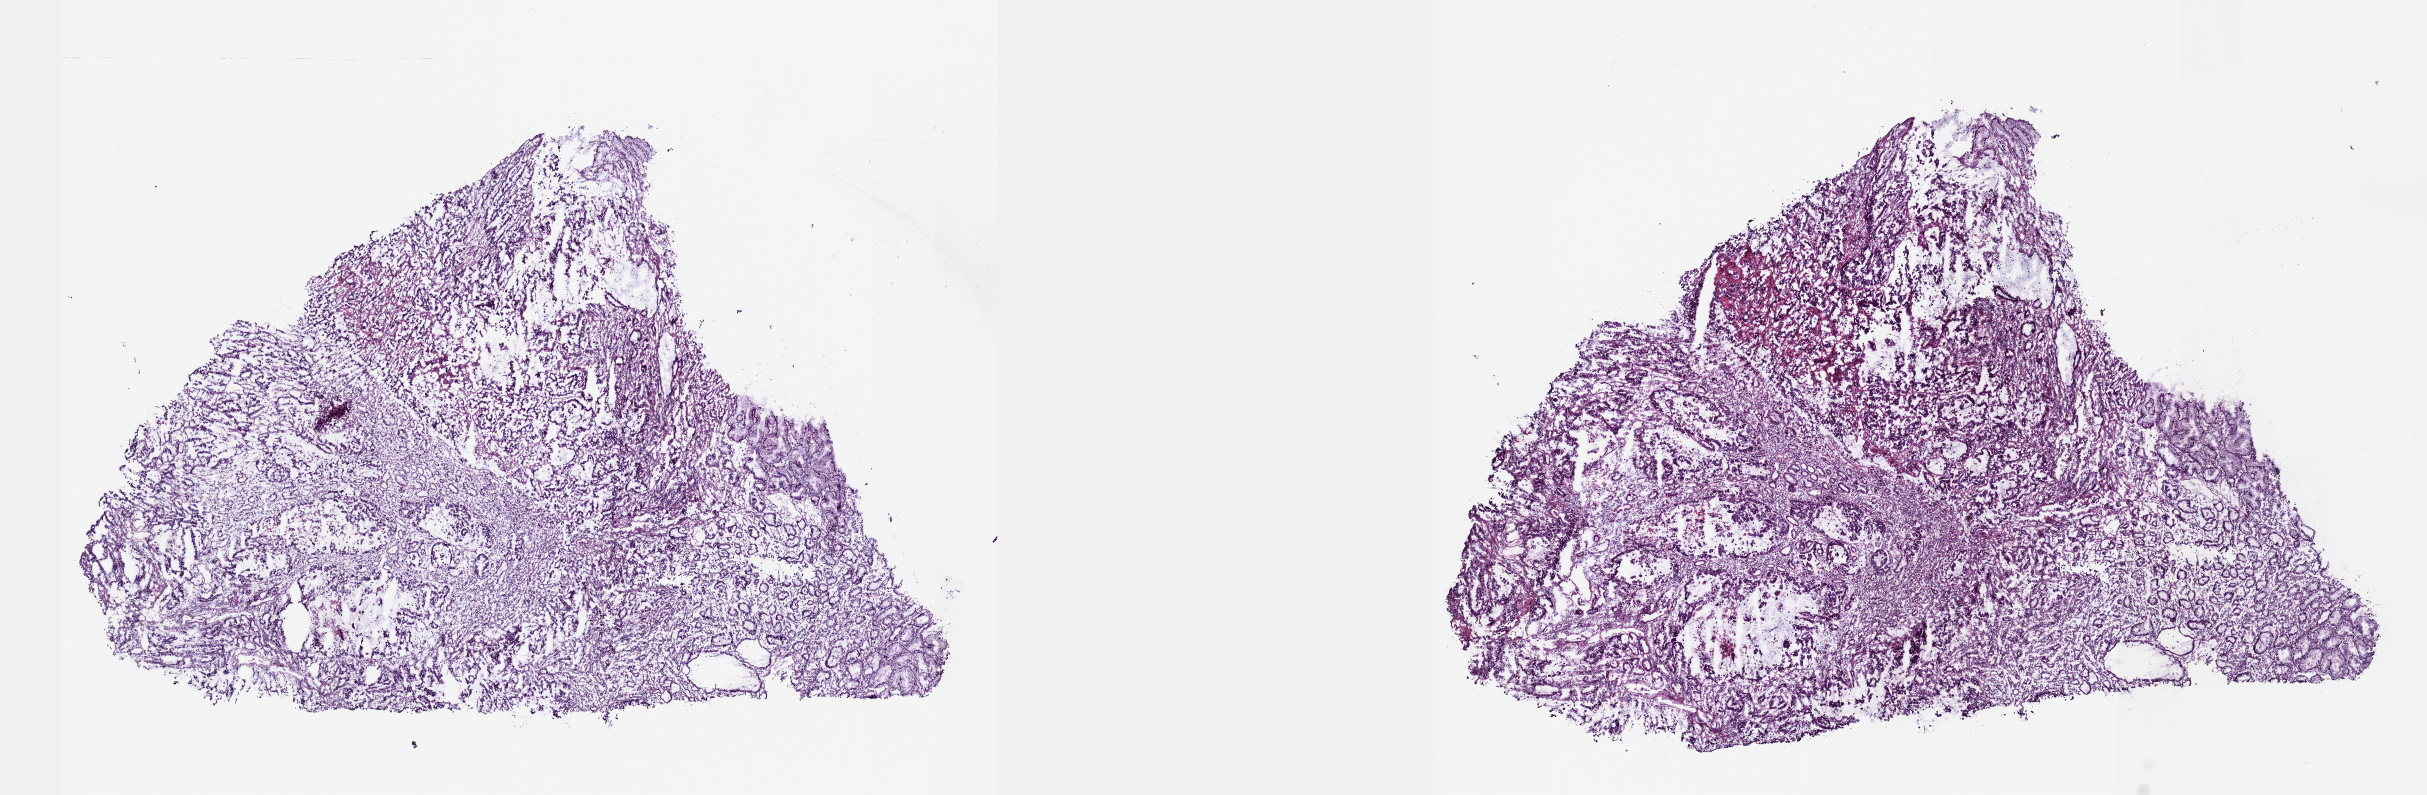
Digitized H&E tissue section (whole slide) — shown as a low-resolution overview of the whole scanned area (about 19.6 x 6.4 mm). Frozen section. Primary tumour sample from the stomach. Male patient; age at initial diagnosis 68 years. Histologic grade: G2 (moderately differentiated). Pathologist review of this section (percent, as recorded): tumour cells 60%, tumour nuclei 60%, normal cells 20%, stromal cells 20%, necrosis 0%. Infiltration values recorded for this section: lymphocyte infiltration 40%, monocyte infiltration 20%, neutrophil infiltration 20%.
* AJCC pathologic stage: IIIB (7th edition)
* histologic diagnosis: Adenocarcinoma, intestinal type